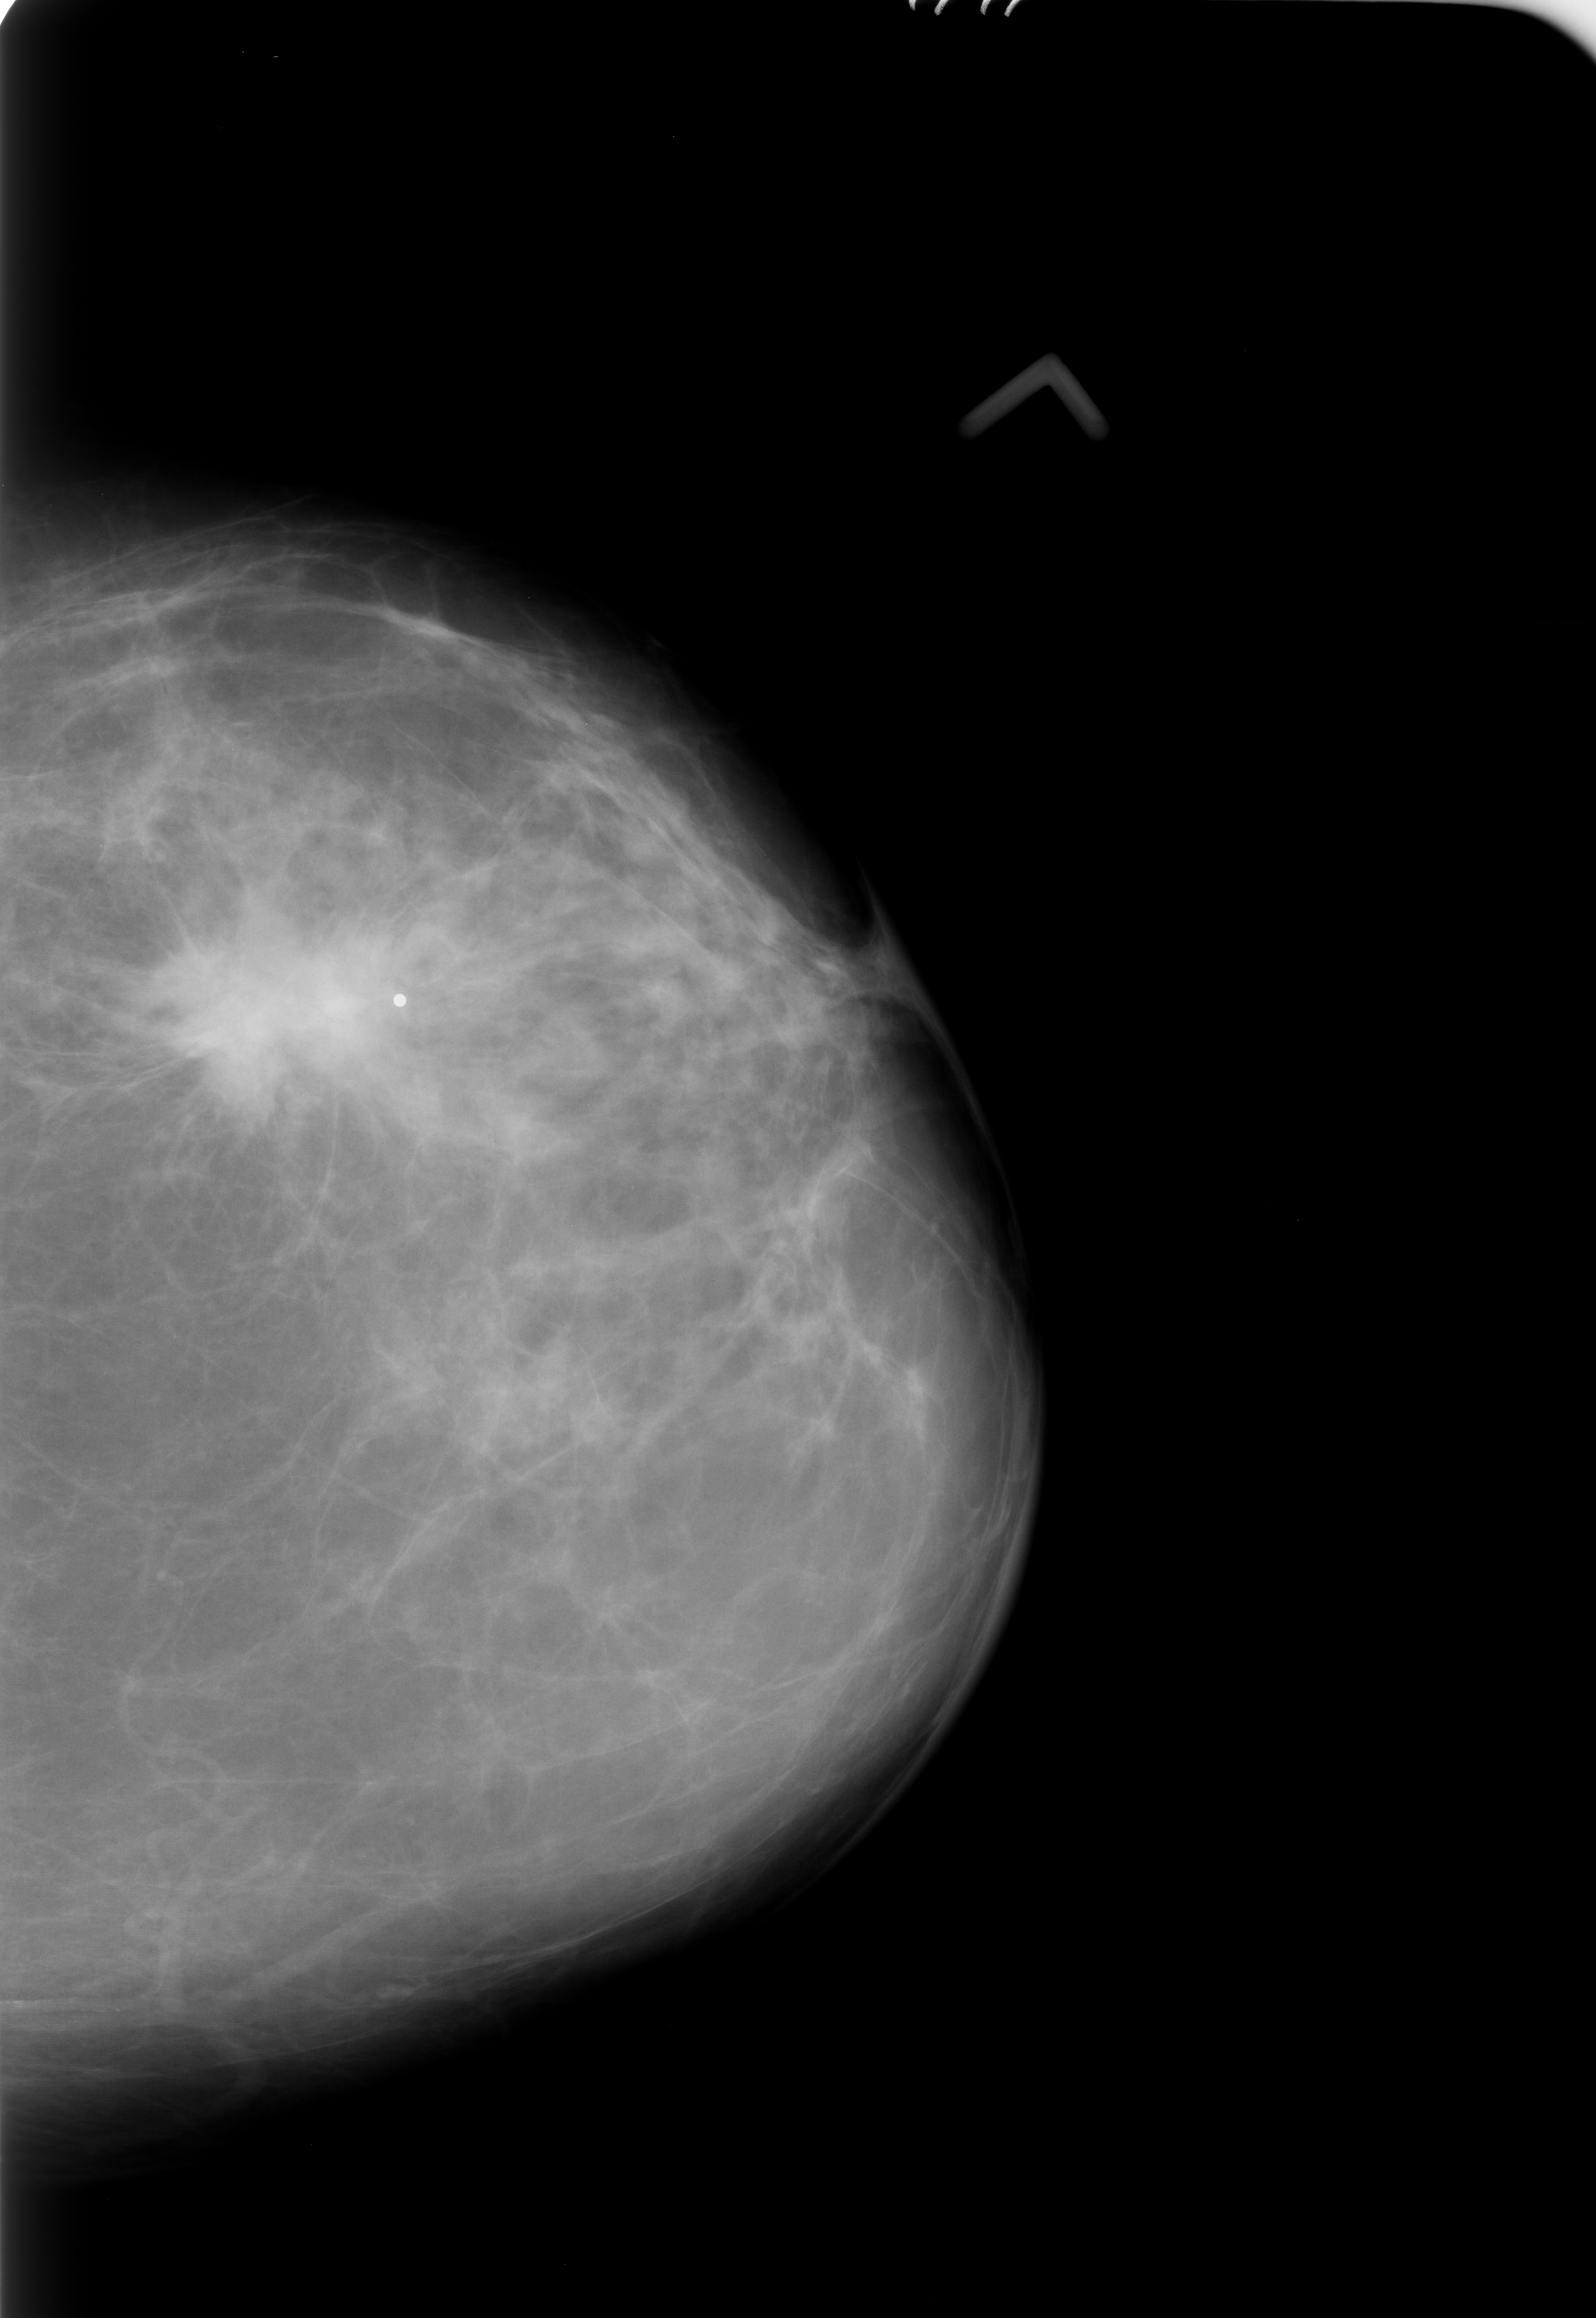
Digitized screen-film mammogram, left breast, CC view, BI-RADS breast density category 2 (scale 1–4).
Mass, shape irregular / architectural distortion, margins spiculated; BI-RADS assessment category 5; subtlety rating 5 on a 1 (subtle) to 5 (obvious) scale; pathology (as recorded): malignant.